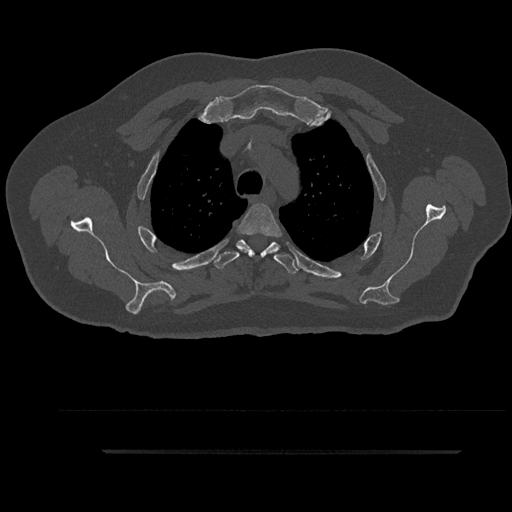
CT including the spine, one axial slice; slice 697 of 797 in the series (ordered by position); reconstruction kernel Br40s/3; 120 kVp; bone window (W 1800 / L 400 HU); 0.5 mm slice thickness; 512 × 512 image matrix, field of view 432 × 432 mm. Male patient, age 63 years. From the clinical record (not read from this slice): primary cancer: renal.
Outlined on this slice (semi-automatically segmented with operator editing):
- T3 vertebra: bounding box [x1, y1, x2, y2] px = [238, 203, 282, 255]
- T4 vertebra: [211, 239, 299, 274]